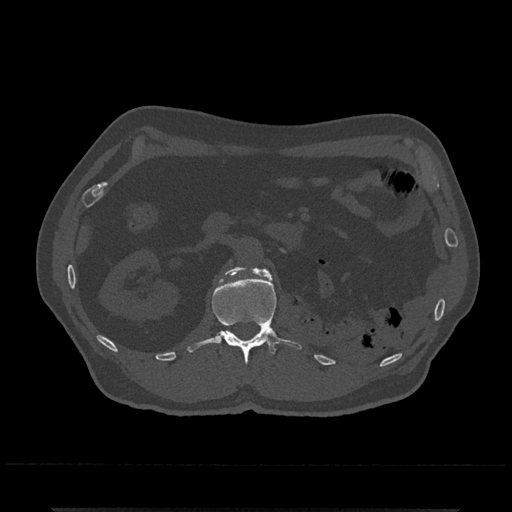
CT including the spine, one axial slice. Position 355 of 797 along the scan axis. Reconstruction kernel Br40s/3. 120 kVp. Bone window (W 1800 / L 400 HU). 0.5 mm slice thickness. 512 × 512 image matrix. Patient: male, 67 years. From the clinical record (not read from this slice): primary cancer: prostate.
Structures marked on this image (semi-automatic segmentation, software-assisted and operator-edited):
- L1 vertebra: bounding box (x1, y1, x2, y2) in pixels: (187, 266, 302, 365)